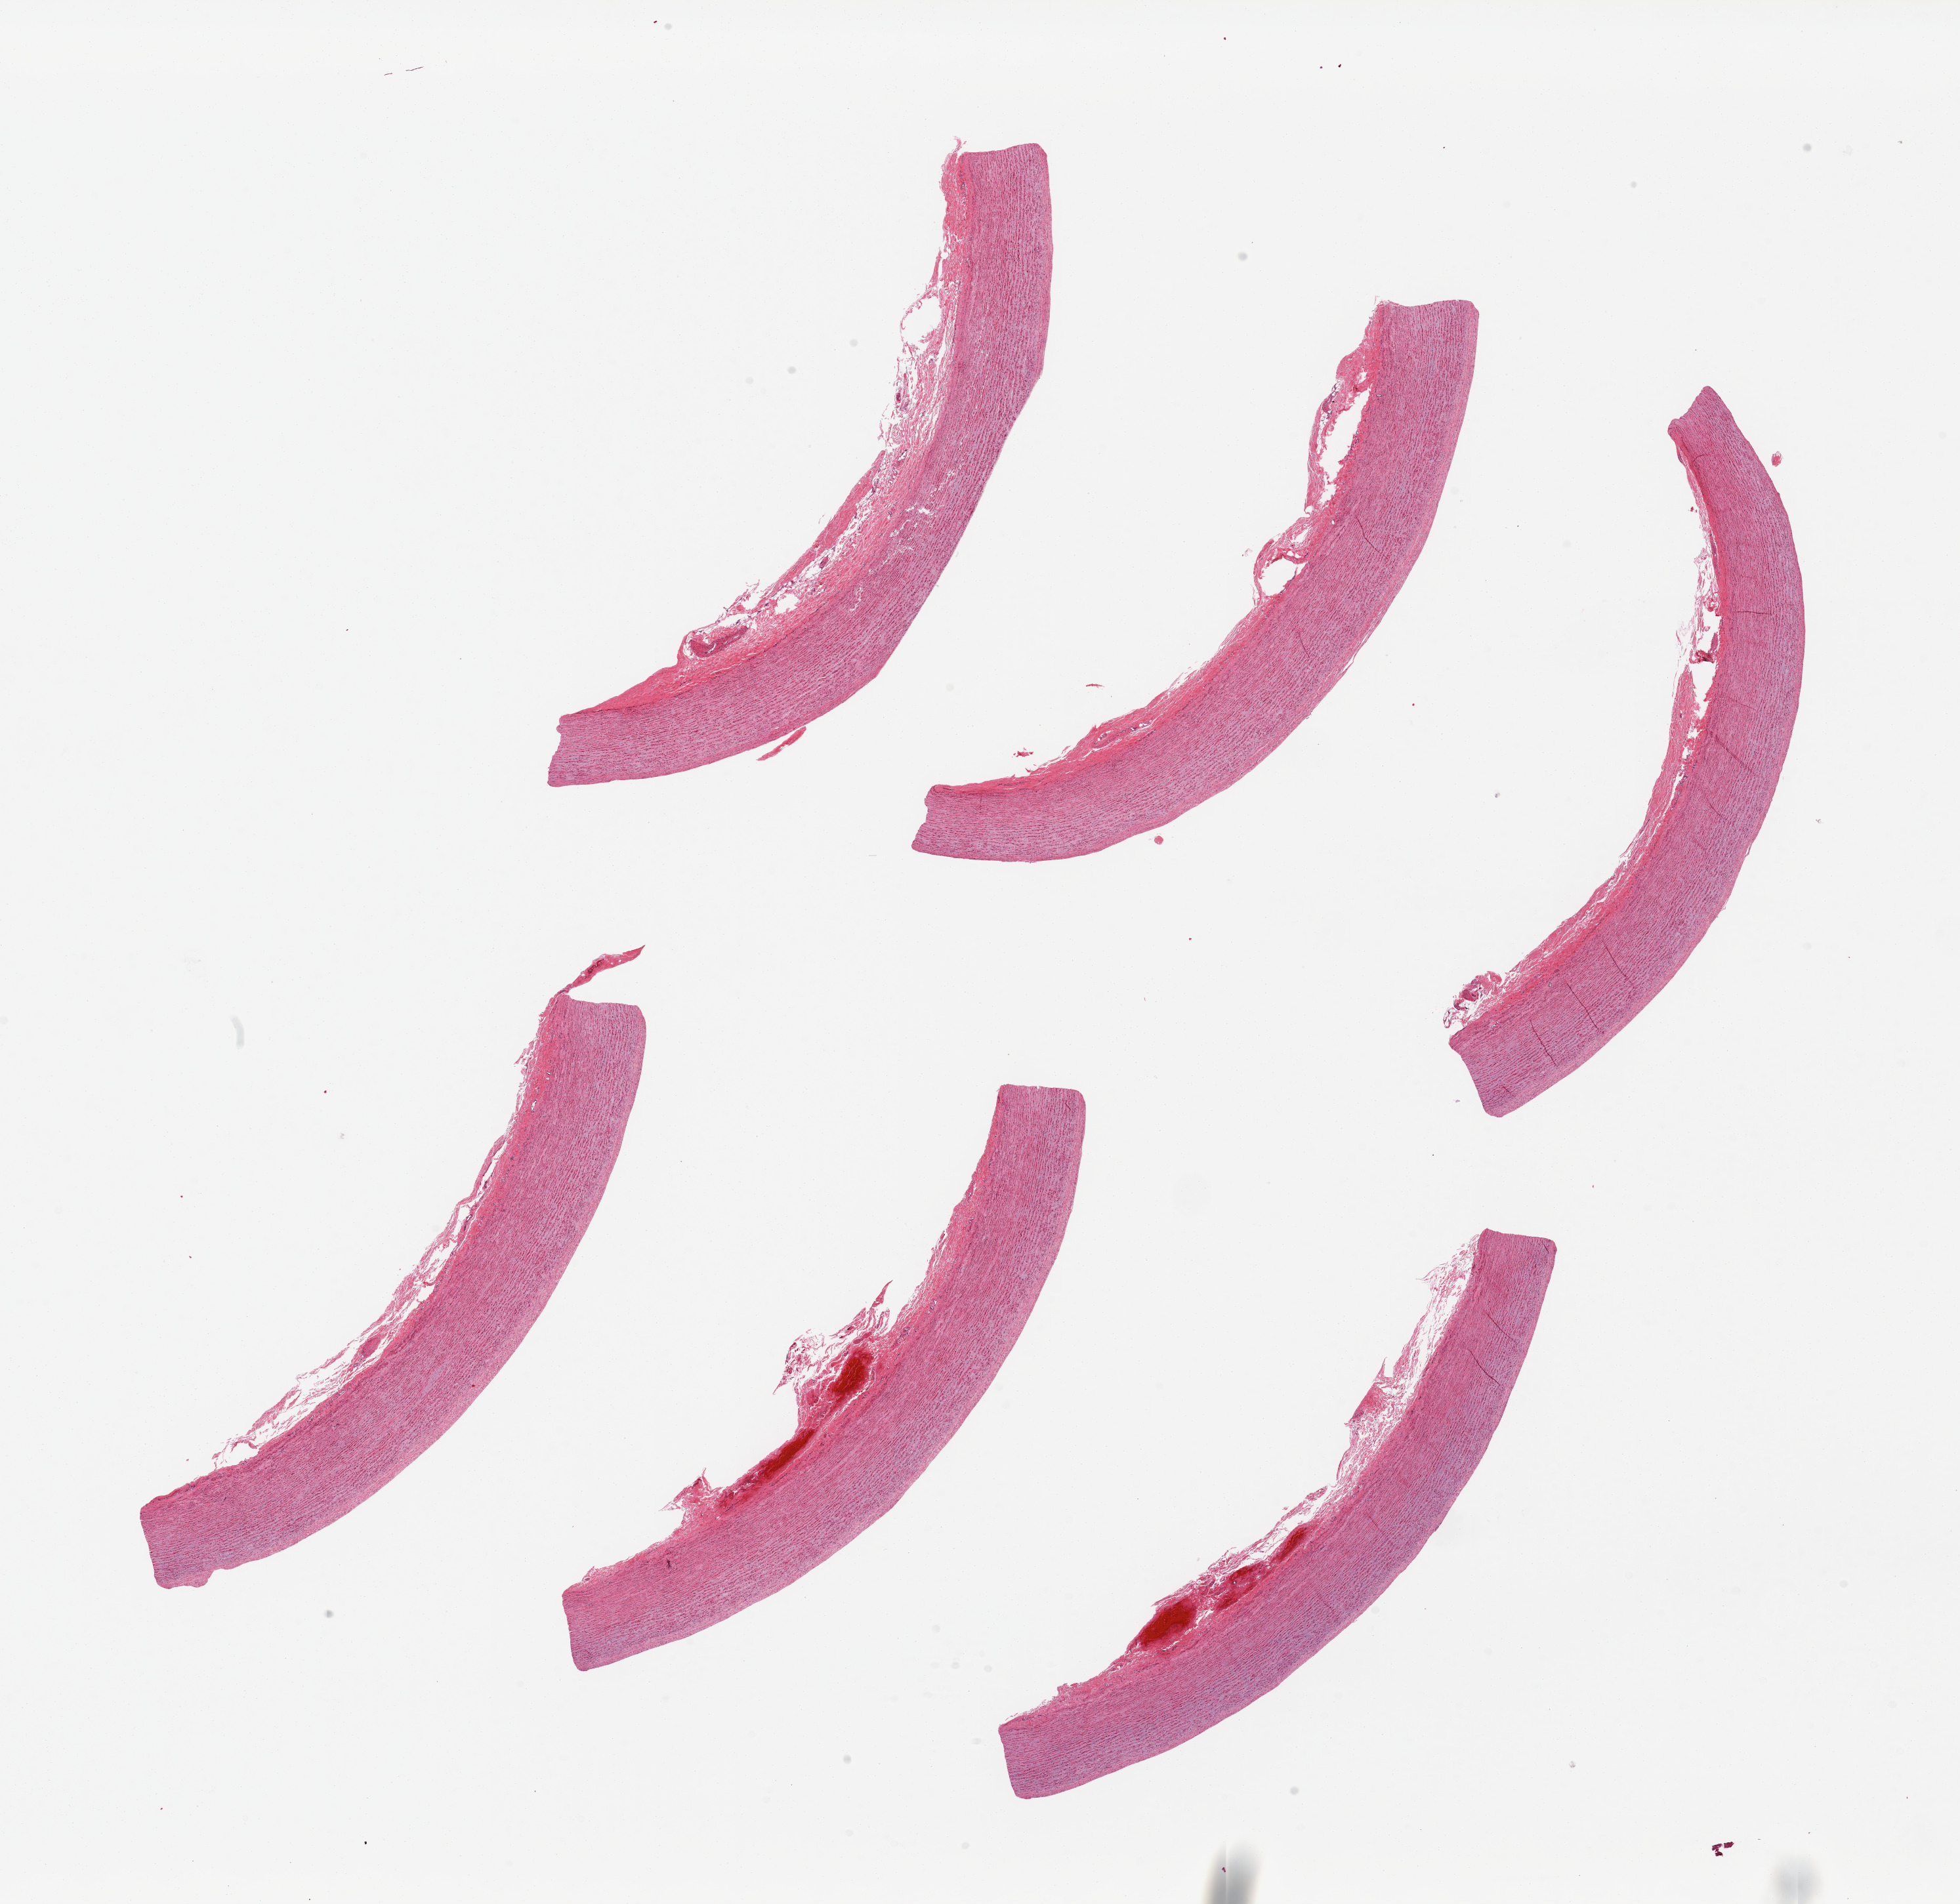
Hematoxylin and eosin (H&E) whole-slide image, brightfield — low-resolution overview of the scanned area, about 23.6 x 23.0 mm, PAXgene-fixed, paraffin-embedded tissue, sampled site (target tissue): aorta, donor tissue sample. Donor sex: male.
* pathologist's review note for this sample: 6 pieces ~9x1.5mm